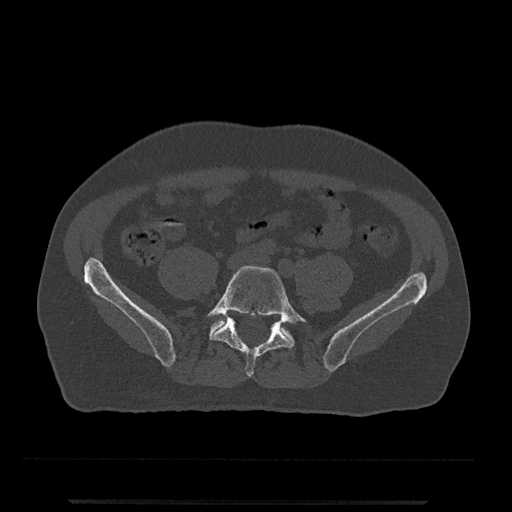
CT including the spine, one axial slice; position 68 of 797 along the scan axis; reconstruction kernel Br40s/3; 120 kVp; bone window (W 1800 / L 400 HU); 512 × 512 image matrix, field of view 419 × 419 mm. Patient: male, 63 years. Case-level facts recorded for this patient, not image findings: primary cancer: prostate.
Structures marked on this image (semi-automatically segmented with operator editing):
- L5 vertebra: bounding box <207,266,307,377> (left, top, right, bottom; pixels)